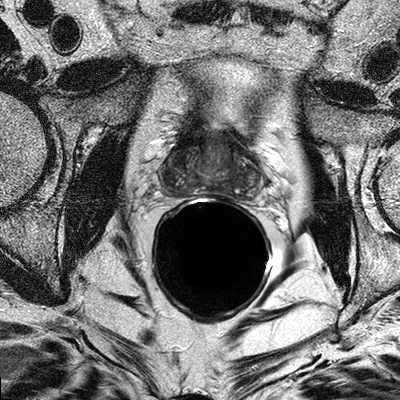
MRI of the prostate; 3 images, each a single mid-volume slice chosen by position (not for content). Treatment context recorded for this patient: No surgery, radical prostatectomy was less desirable due to his age, patient is contemplating other treatment options.
Image 1: axial T2-weighted image, slice 17 of 32, 3 mm slice thickness.
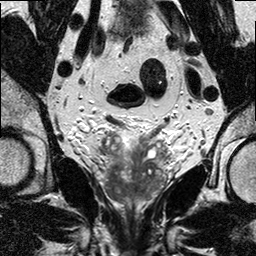
Image 2: coronal T2-weighted image, series "T2W_TSE_COR", slice 13 of 24.
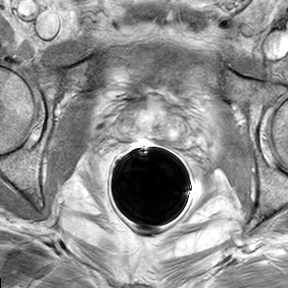
Image 3: DCE (dynamic gadolinium-enhanced) axial slice, slice 17 of 32, dynamic phase 5 of 8, 6 mm slice thickness.
Radiologist's MRI report for this examination:
prostate has a maximal lateral diameter of 4.8 cm, a maximal craniocaudal diameter of 3.8 cm and a maximal AP diameter of 3.2 cm resulting in an estimated gland volume of 30 cc. The zonal anatomy is preserved. There is a 1.5 x 0.9 cm T-2 W hypointense mass seen in the right posterior-lateral peripheral zone in the mid third of the prostate extending into the apex of the prostate, with suspicious enhancement (rapid wash in and out).This nodule abuts the capsule at the level of mid third and apical third, however there is no extraprostatic tumor or enhancement seen at that levels. At the right posterior lateral apex there asymmetric irregular T2-W hypointense tissue with suspicious enhancement seen, with indistinct borders to the surrounding fatty tissue: beginning extraprostatic extension right posterior lateral at the apex of the prostate possible. There are several small sub 5 mm areas of indeterminate enhancement seen in the left peripheral zone of the mid and upper third of the prostate, therefore multifocality possible, however the dominant nodule clearly on the right side, and these small areas could also represent chronic prostatitis. No evidence for involvement of the neurovascular bundle on either side. No definite seminal vesicles infiltration. No evidence of involvement of bladder neck and rectal wall. There are several up to 9 mm rounded lymph nodes seen on the iliac levels on both sides, beginning just above the obturator muscles up to the bifurcation. Some show a fatty hilum. IMPRESSION: 1) Right sided prostate cancer with the dominant nodule (1.5 x 0.9 cm) in the midthird and apical third of the prostate in the posterior lateral peripheral zone. Possible beginning extraprostatic extension at the posterior lateral right apex. Several up to 9 mm iliac lymph nodes bilateral, of unknown significance. No evidence of seminal vesicle infiltration or involvement of bladder neck or rectum. 2) BPH, Chronic prostatitis.

Biopsy pathology report for this patient (as recorded):
Specimen consists of multiple brown/tan core biopsies measuring in length from 0.3 cm to 2 cm and 0.01 cm in diameter each. The specimen is submitted in toto in six cassettes as follows: 1 right PZ, 2 right PZ/TZ, 3 right apex, 4 left PZ, 5 left PZ/TZ, 6 left apex. Final Diagnosis PROSTATIC CORE NEEDLE BIOPSIES: 1. RIGHT PZ: PROSTATIC TISSUE. NO TUMOR IDENTIFIED. 2. RIGHT PZ/TZ: PROSTATIC ADENOCARCINOMA, GLEASON SCORE (3+4) =7/10, PRESENT IN APPROXIMATELY 30% OF THE TISSUE SUBMITTED. 3. RIGHT APEX: PROSTATIC ADENOCARCINOMA, GLEASON SCORE (3+3) =6/10, PRESENT IN LESS THAN 5% OF THE TISSUE SUBMITTED. 4. LEFT PZ: PROSTATIC TISSUE WITH MILD CHRONIC INFLAMMATION. NO TUMOR IDENTIFIED. 5. LEFT PZ/TZ: SINGLE MICROSCOPIC ATYPICAL GLANDULAR FOCUS. 6. LEFT APEX: SCANT PROSTATIC TISSUE. NO TUMOR IDENTIFIED.